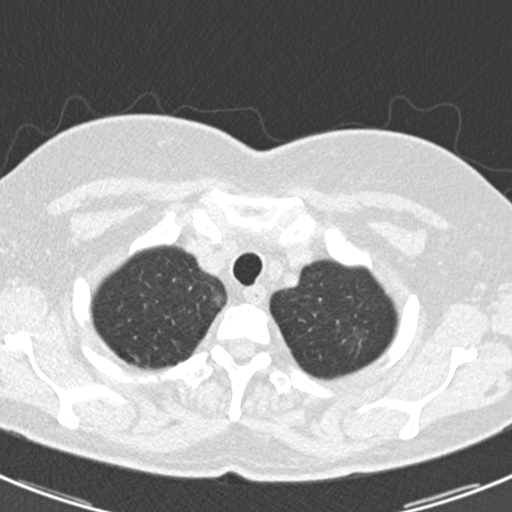
Axial slice from a low-dose chest CT screening exam; baseline annual screen; lung window (W 1500 / L -600 HU); 2 mm slice thickness; standard (soft-tissue) reconstruction kernel (B30f); 120 kVp. Female, age 60 years at enrolment. Current smoker at enrolment.
Expert-annotated lung lesion, bounding box [x1, y1, x2, y2] px = [335, 316, 385, 364]. The screening reader recorded 3 non-calcified nodules or masses ≥4 mm on this exam; which of them this box marks is not recorded.